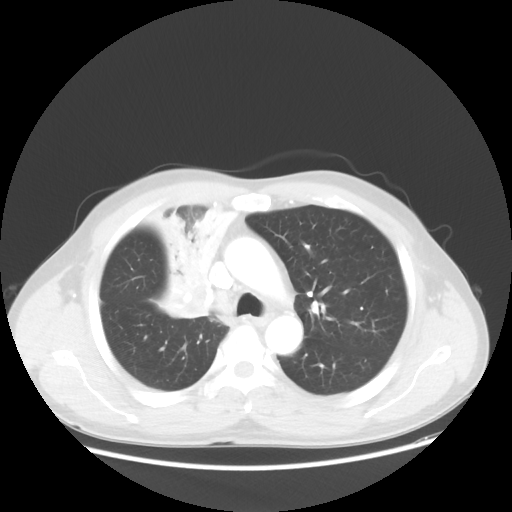
Chest CT, one axial slice; slice 37 of 56 in the series (ordered by position); lung window (W 1500 / L -600 HU); 5 mm slice thickness; 512 × 512 image matrix, field of view 398 × 398 mm. Patient: male, 60 years. From the clinical record (not read from this slice): clinical TNM (as recorded): T2a N1 M0.
Structures marked on this image (rectangle marked by the reading radiologist):
- lung tumour (recorded histology: squamous cell carcinoma): bounding box [x1, y1, x2, y2] px = [140, 196, 237, 326]